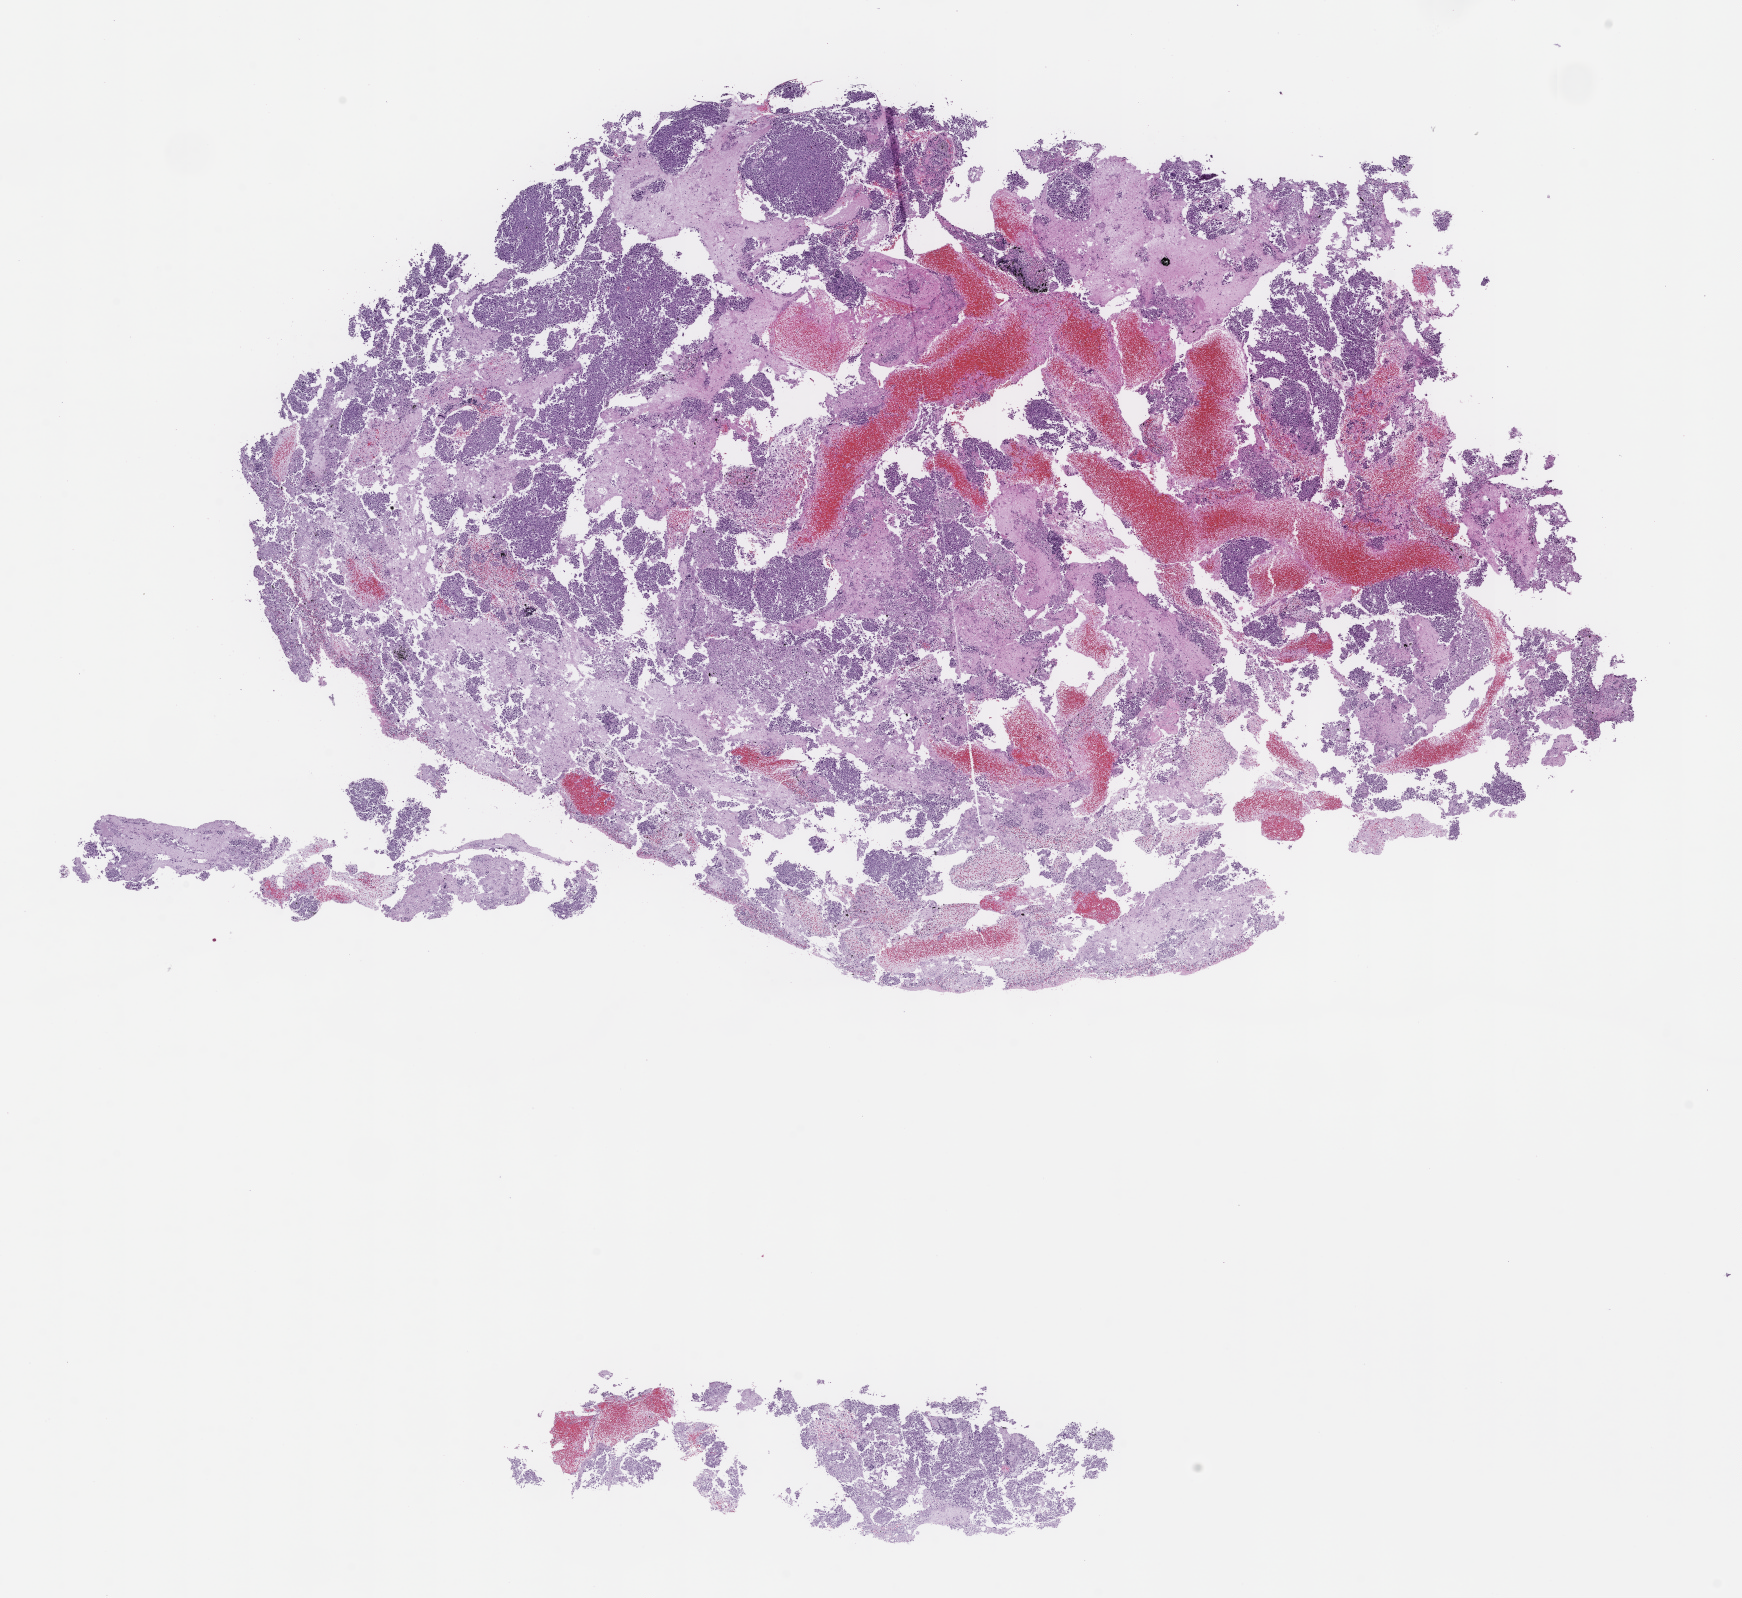
Whole-slide image, H&E stain — a low-resolution overview of the entire scanned area, about 14.1 x 12.9 mm, FFPE section, specimen time point: archival tissue. Patient: female.
This section: metastasis (sampled organ not recorded). Patient diagnosis (primary): Non-Small Cell Lung Carcinoma.